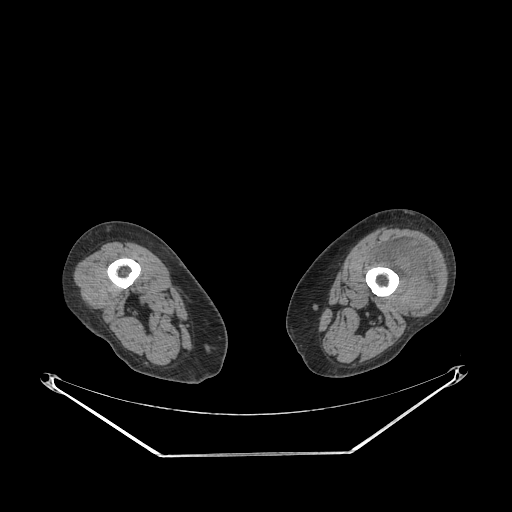
CT of an extremity soft-tissue mass (from a PET/CT study), one axial slice. Slice 203 of 267 in the series (ordered by position). 140 kVp. Soft-tissue window (W 400 / L 40 HU). 512 × 512 image matrix, field of view 500 × 500 mm. Female patient. From the clinical record (not read from this slice): histological type: undifferentiated – high grade; grade: high; site of the primary tumour: left thigh.
Outlined on this slice (expert contour drawn on MRI and transferred to this co-registered scan by the dataset authors):
- gross tumour volume including surrounding oedema: bounding box [x1, y1, x2, y2] px = [370, 240, 435, 312]
- gross tumour volume (mass): [404, 251, 430, 312]